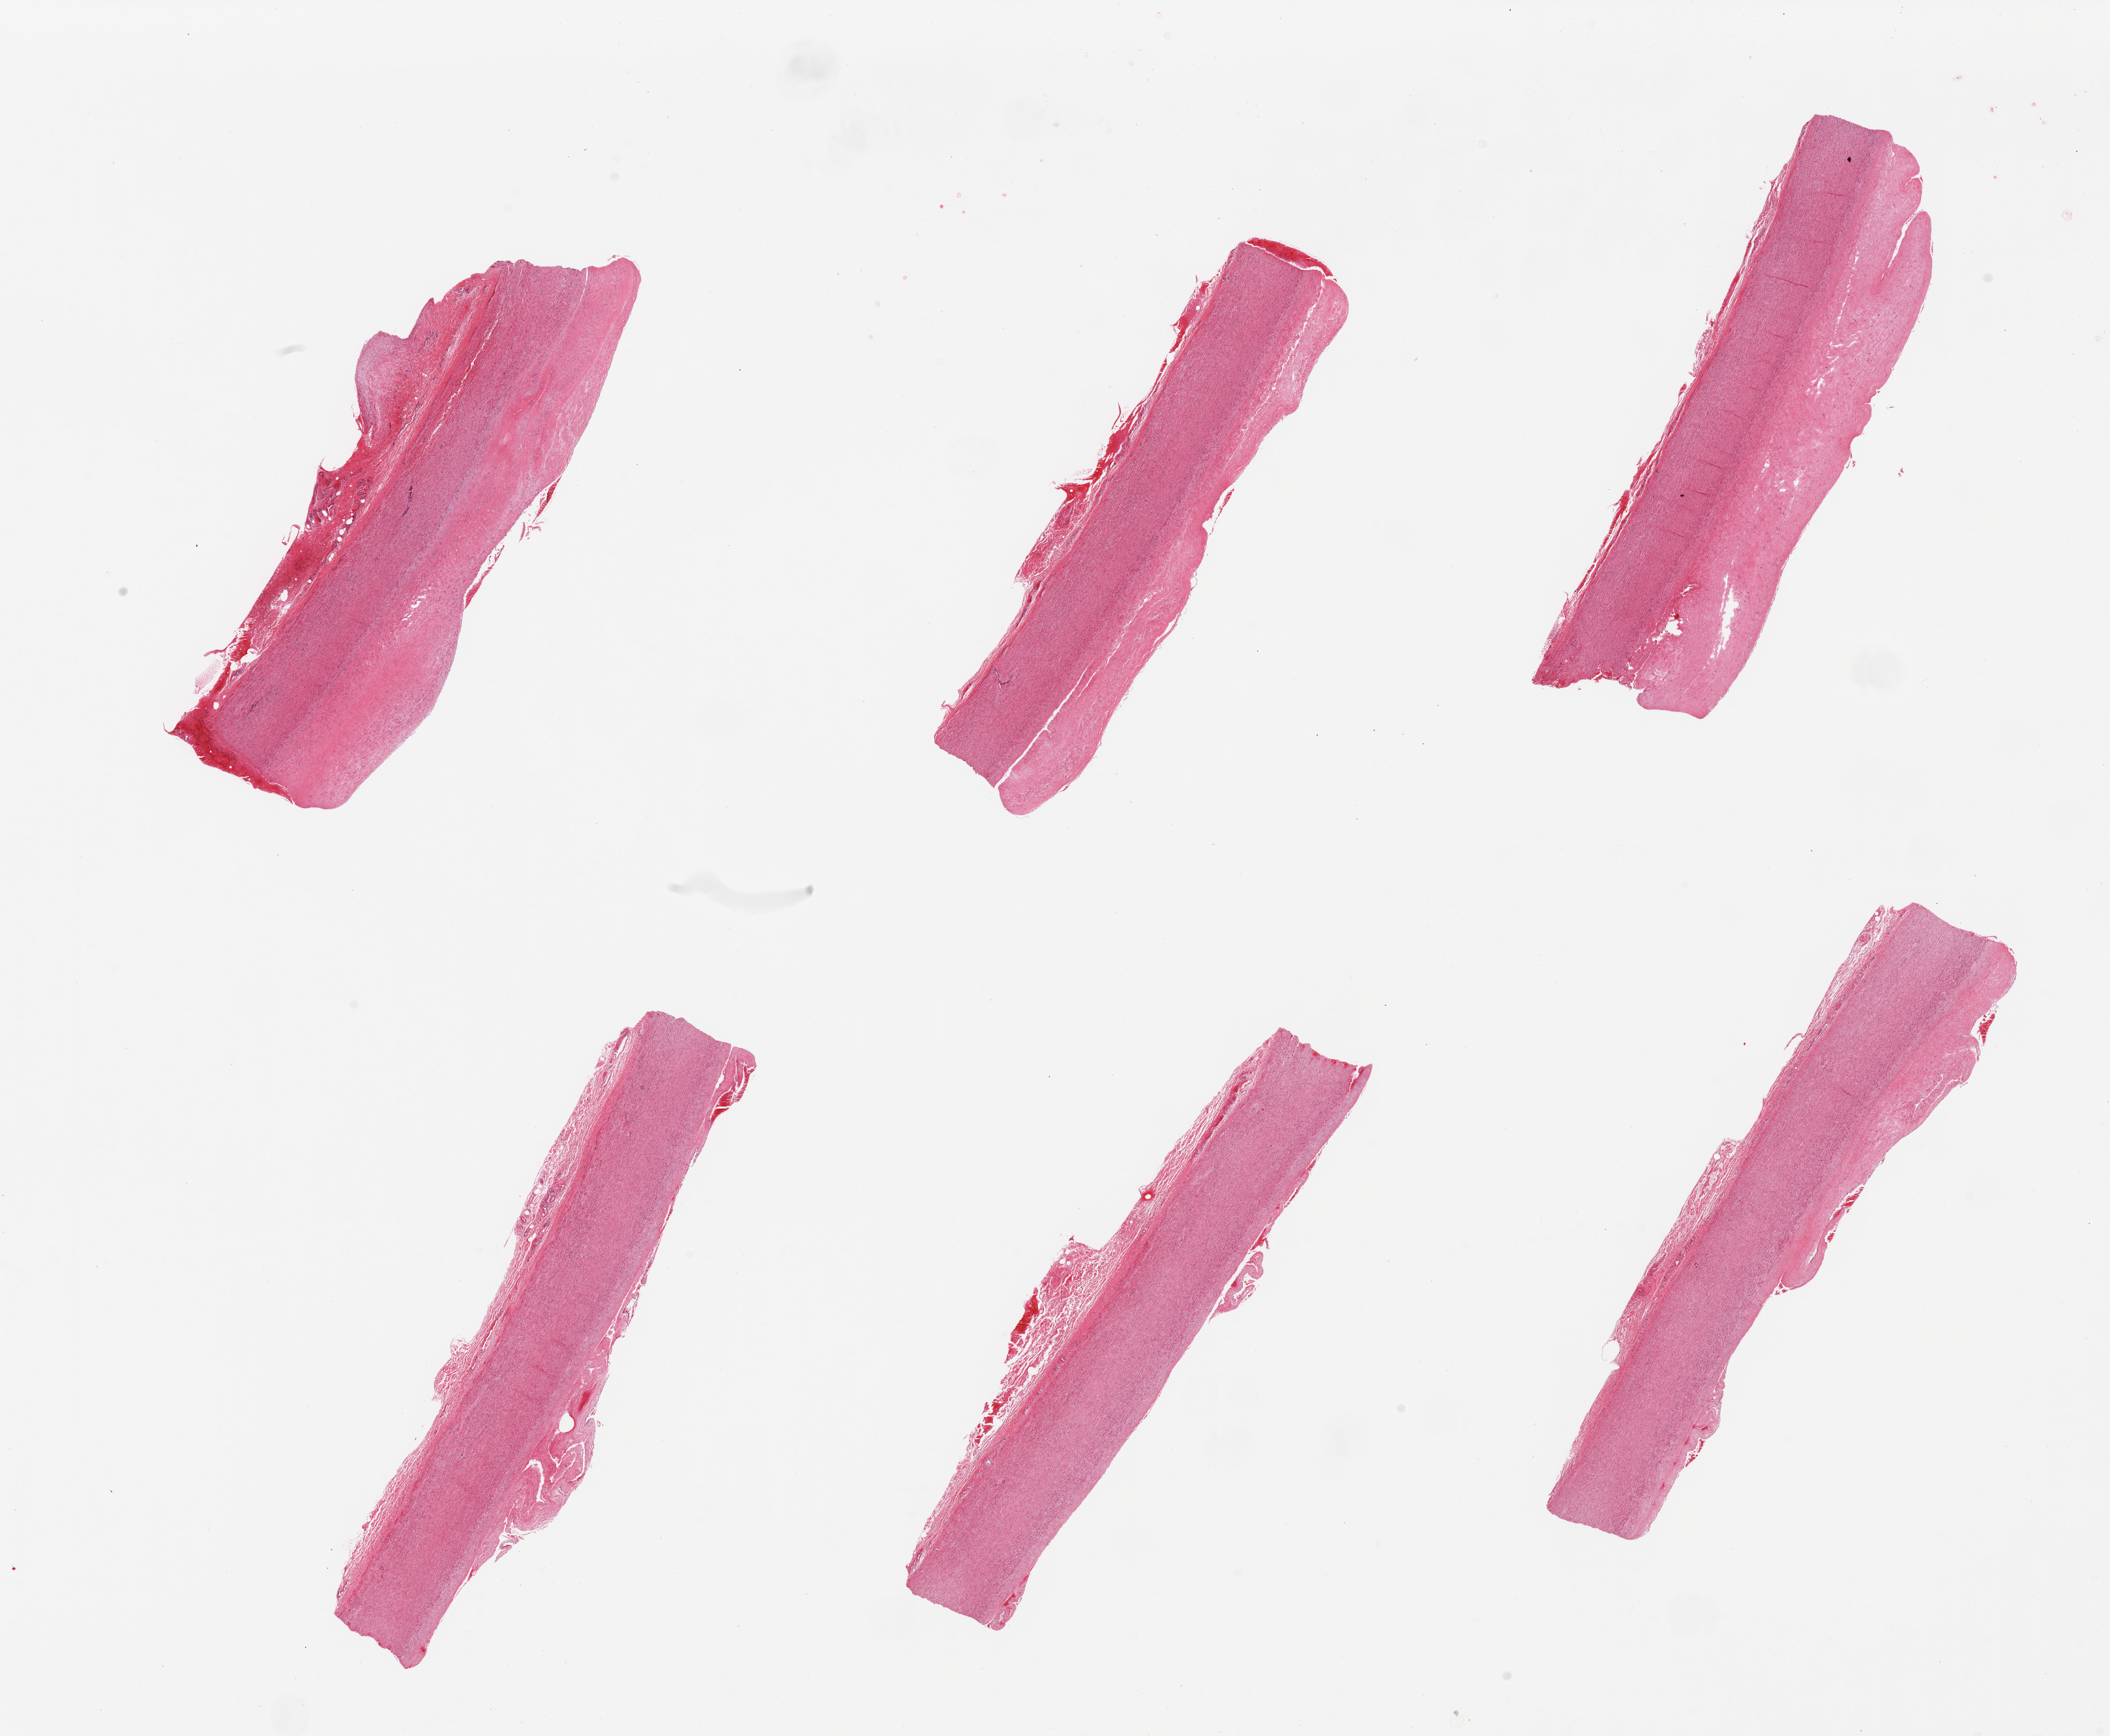
H&E whole-slide image, low-resolution overview of the scanned area, about 25.6 x 21.1 mm. PAXgene-fixed paraffin-embedded (PFPE) section. Section of aorta (target tissue). Donor tissue sample.
Review note (as recorded): 6 pieces. Well trimmed. Intimal plaques up to 0.8mm thick.